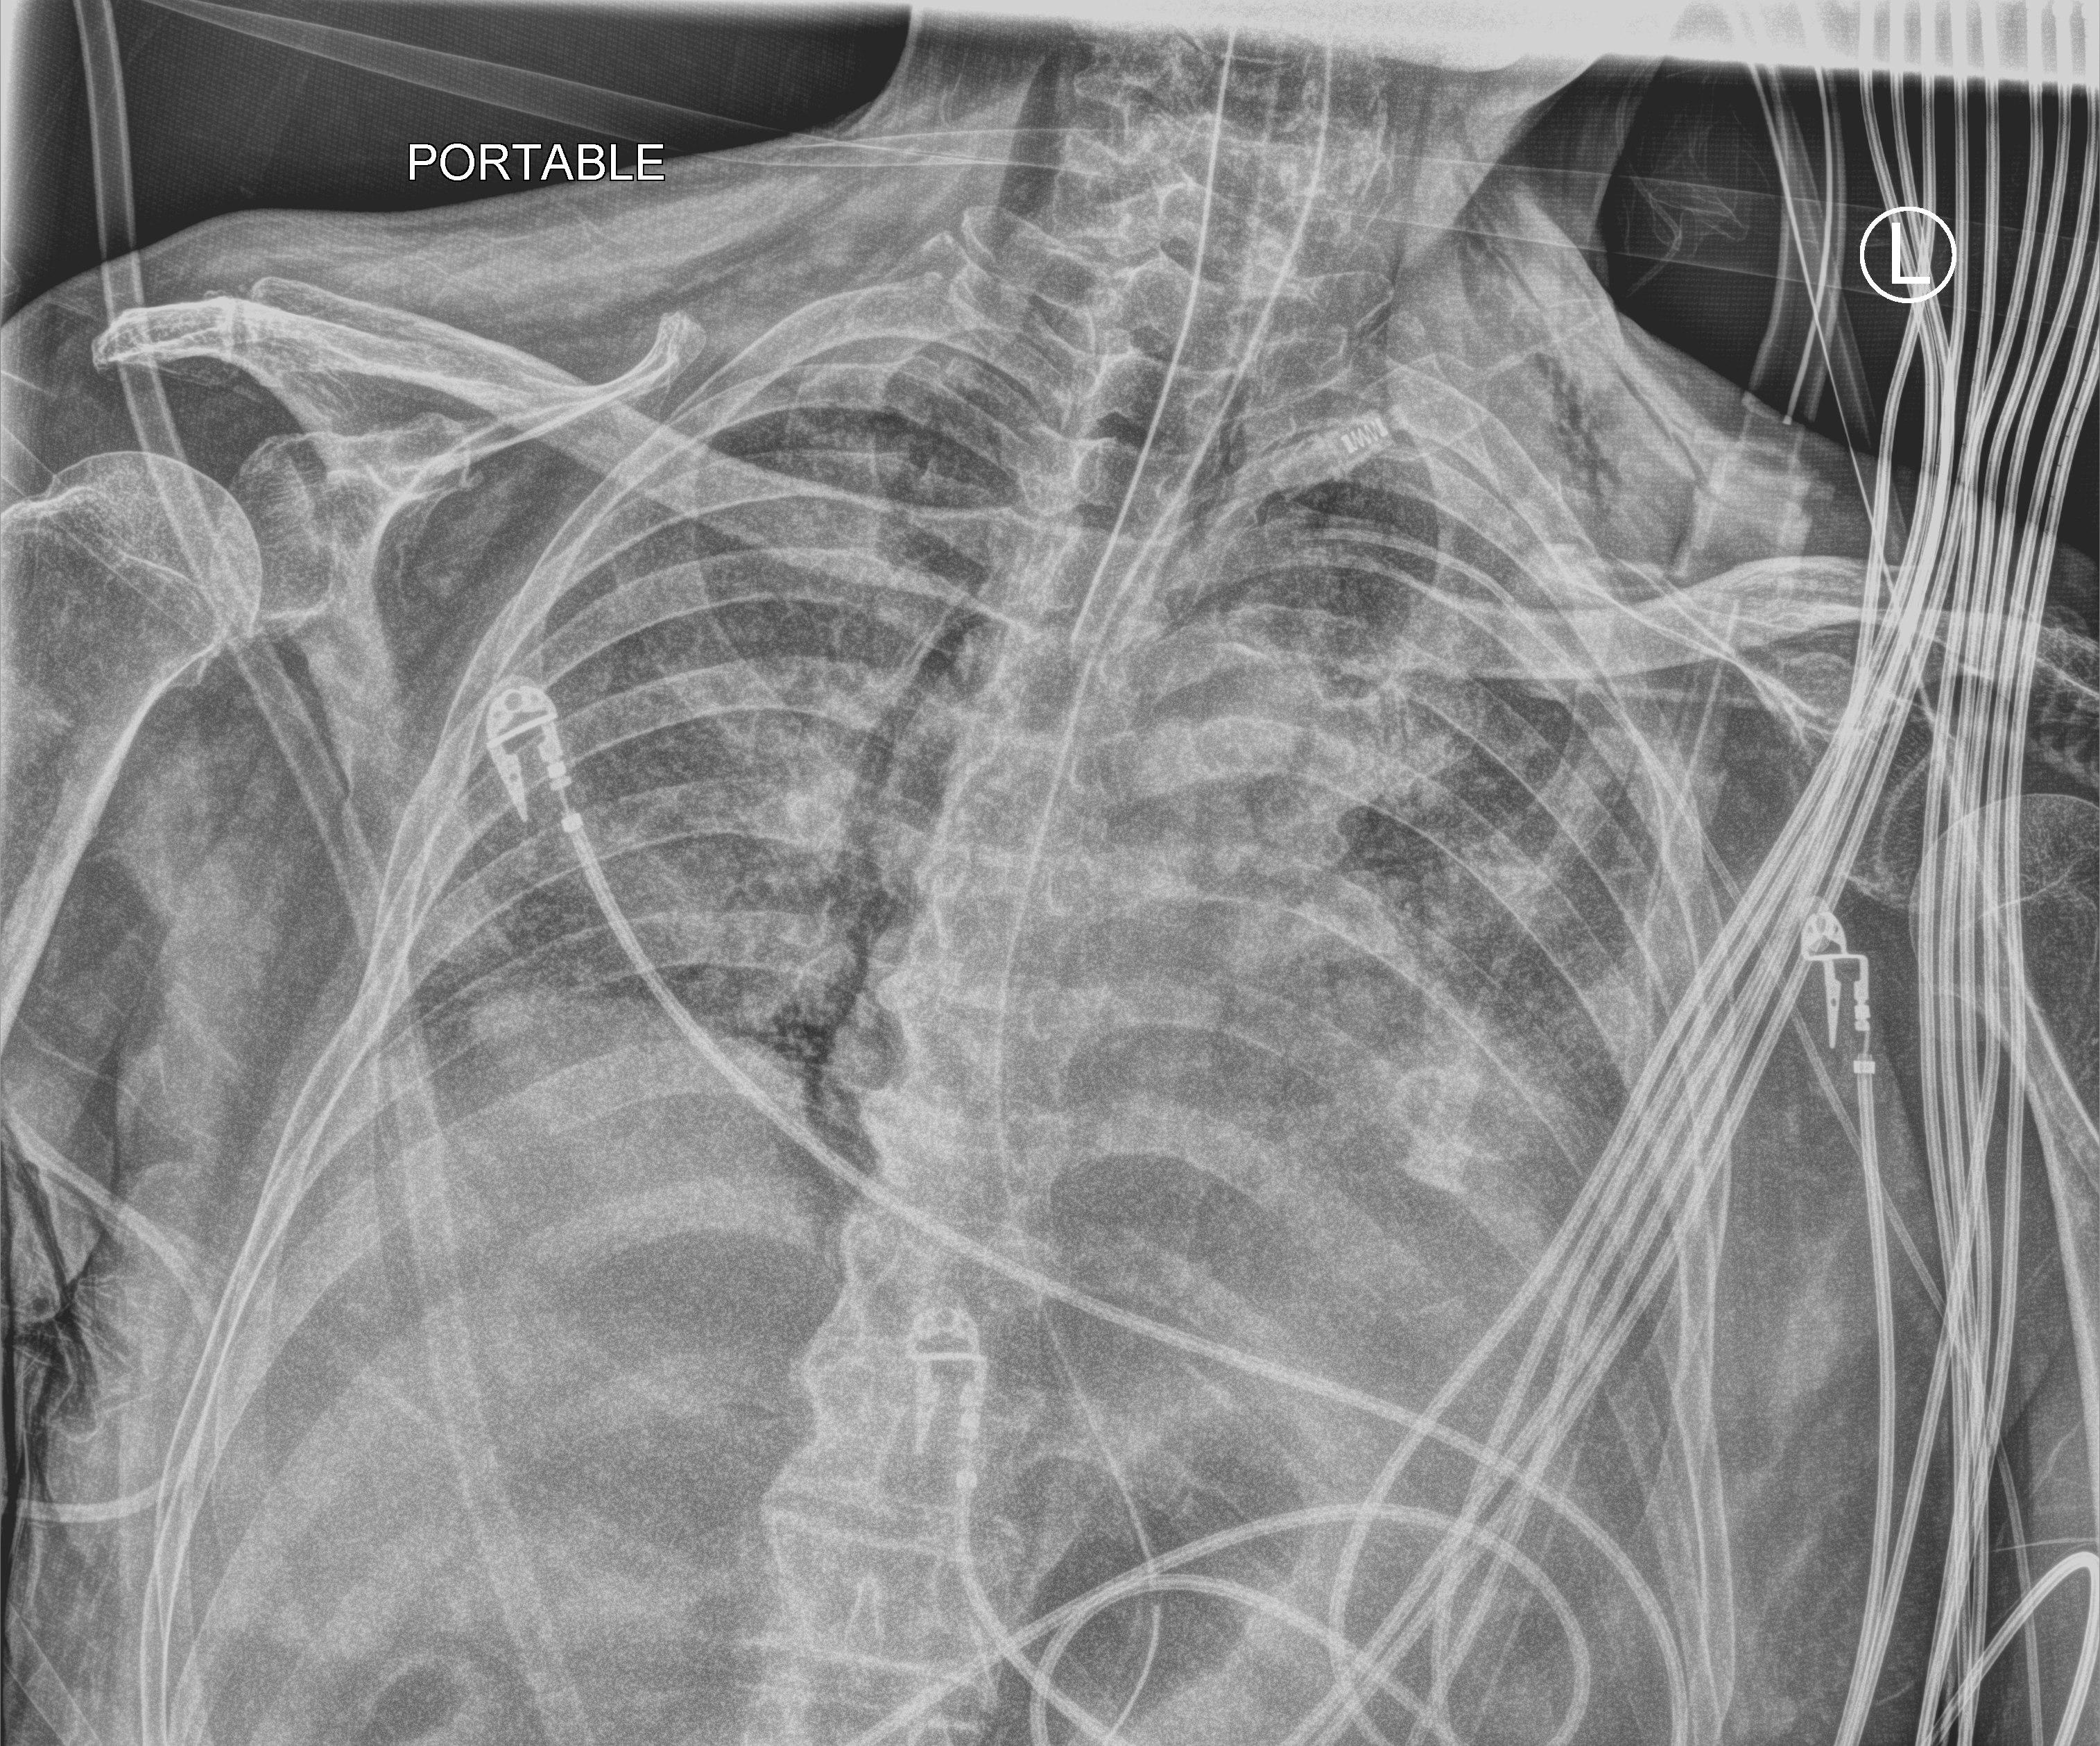
Chest X-ray (portable). Patient hospitalised with COVID-19; male, aged 75–90 years.
From the hospital-stay record, not from the radiograph (when in the stay this image was taken is not recorded): diabetes (admission record): no; smoking status (admission record): never.